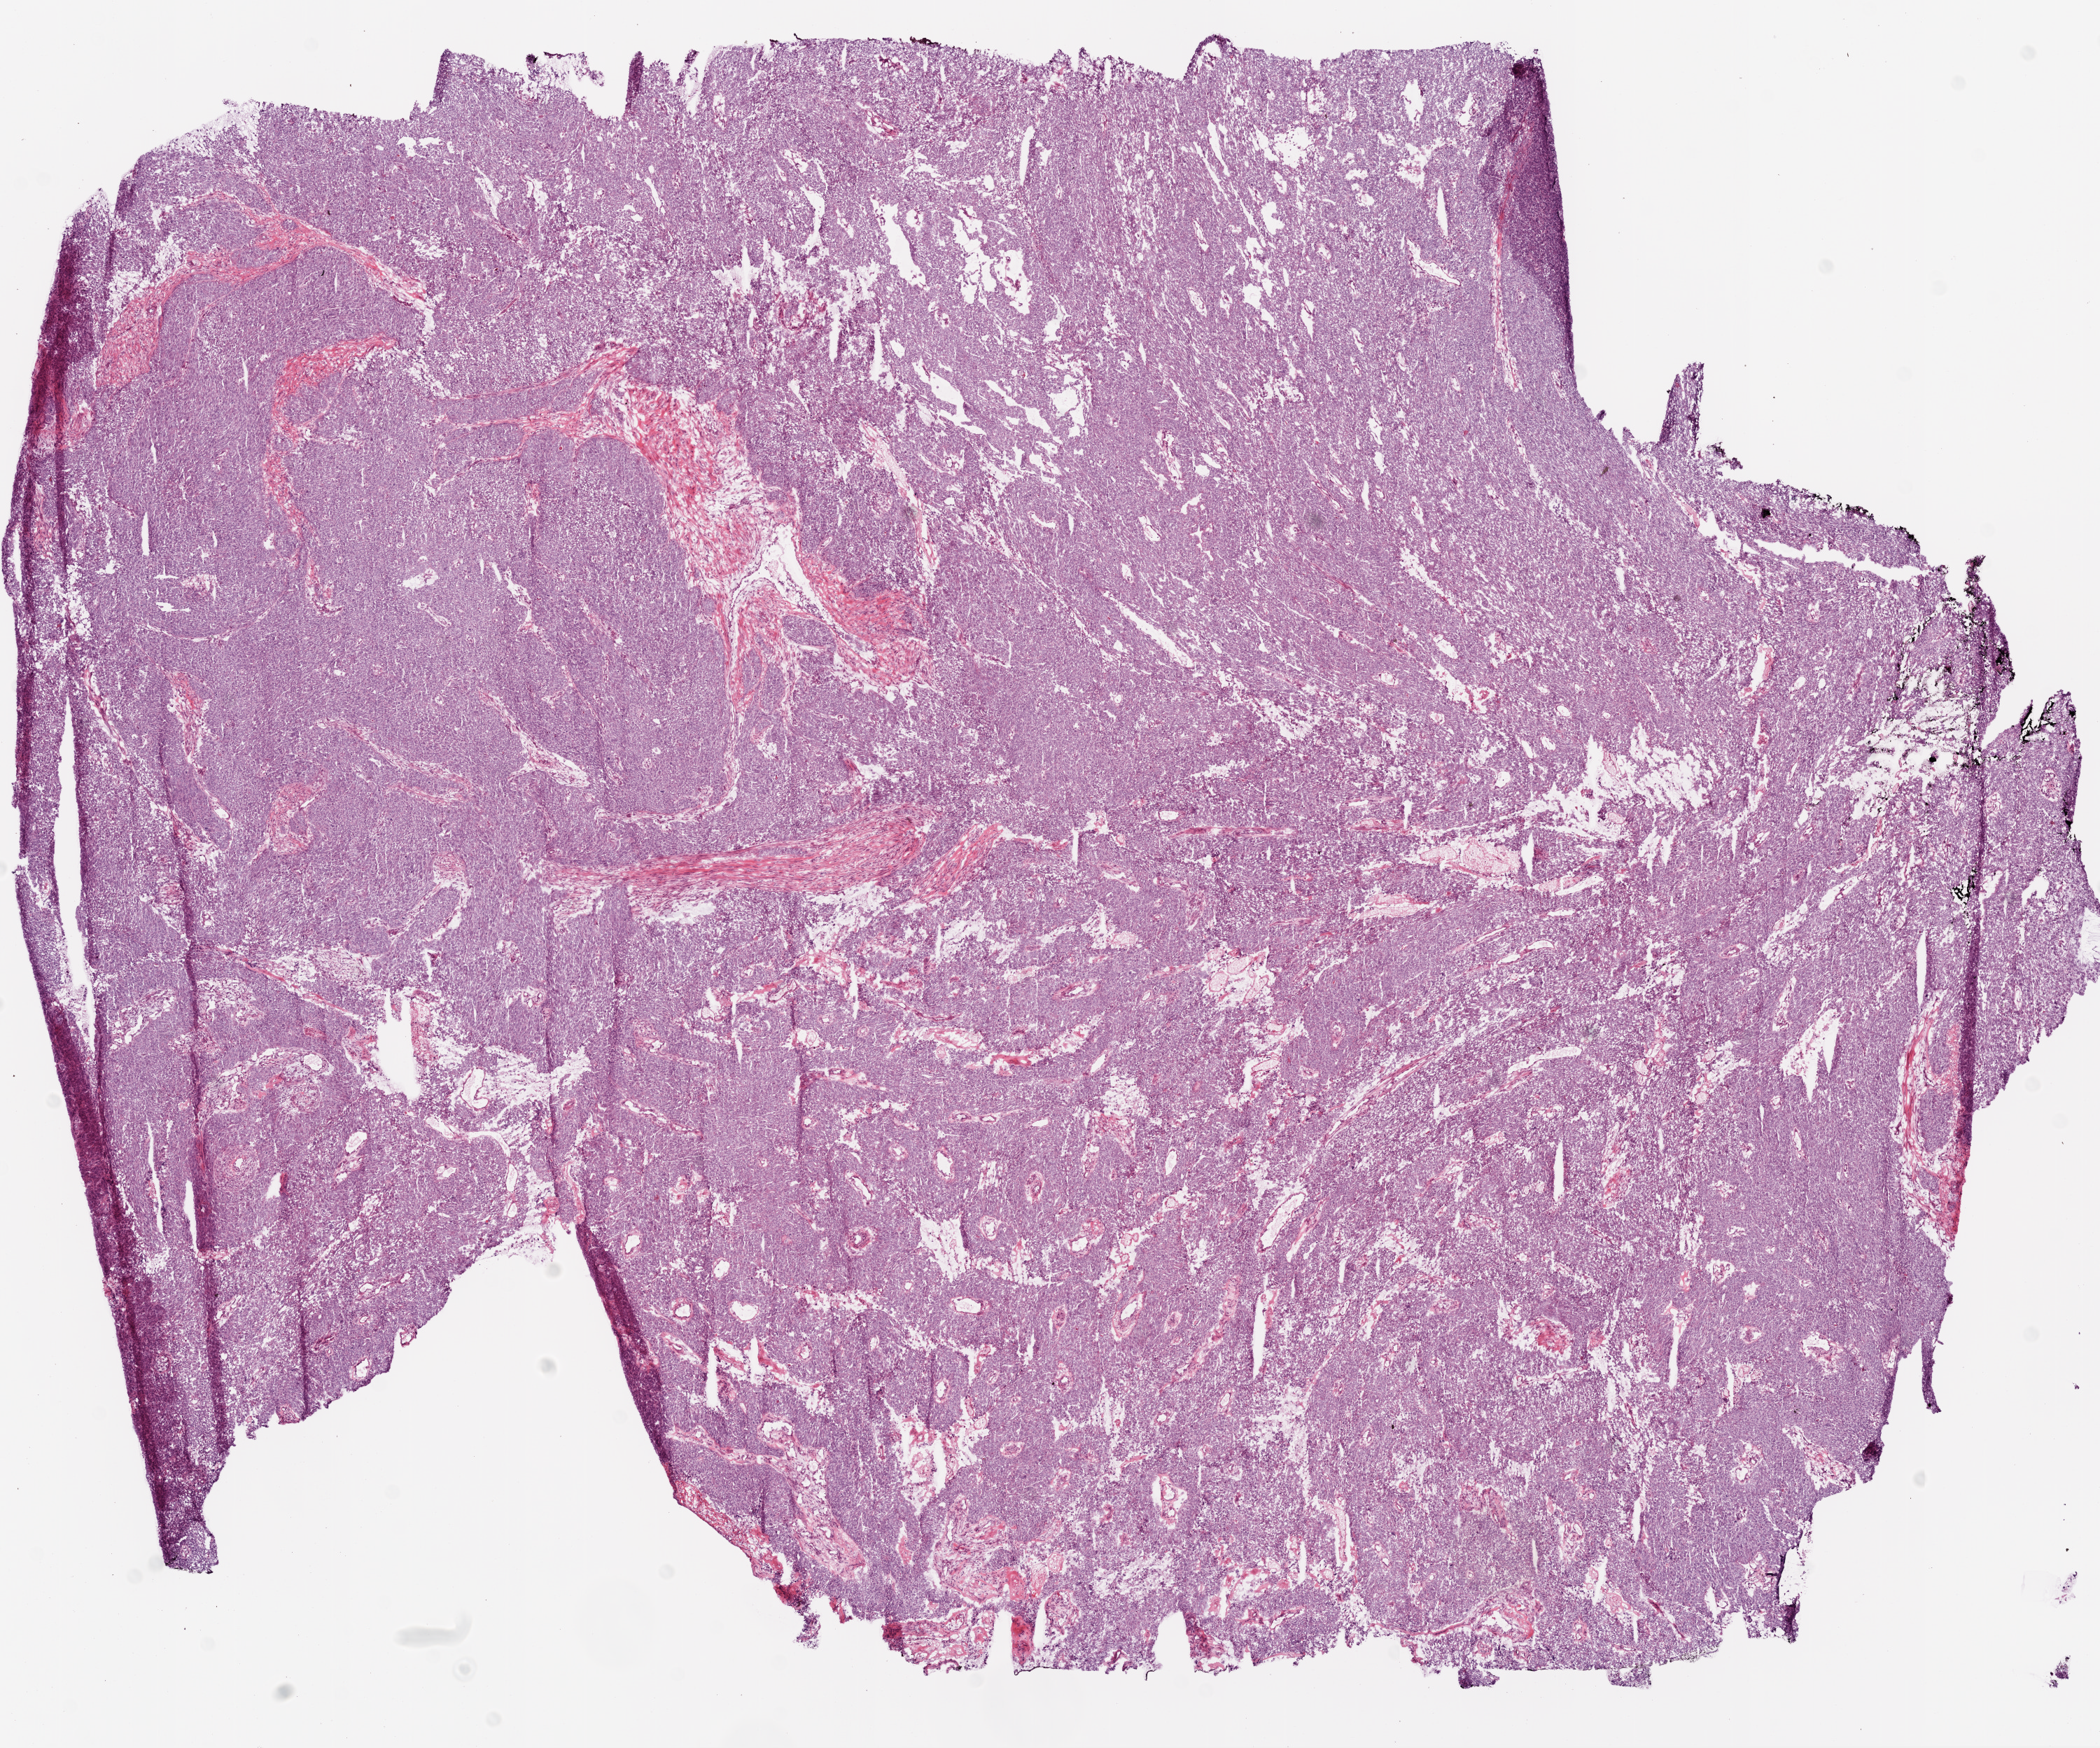
H&E whole-slide image, low-resolution overview of the scanned area, about 12.0 x 10.0 mm (slide scanned at 20x), frozen section, ovary, primary tumour sample. Patient: female, age at initial diagnosis 57 years. Histologic grade: G3 (poorly differentiated). Slide review estimates, as recorded: tumour cells 94%, tumour nuclei 95%, normal cells 0%, stromal cells 10%, necrosis 1%.
Histologic diagnosis: Serous cystadenocarcinoma, NOS. FIGO stage: IIIC. Laterality: left.